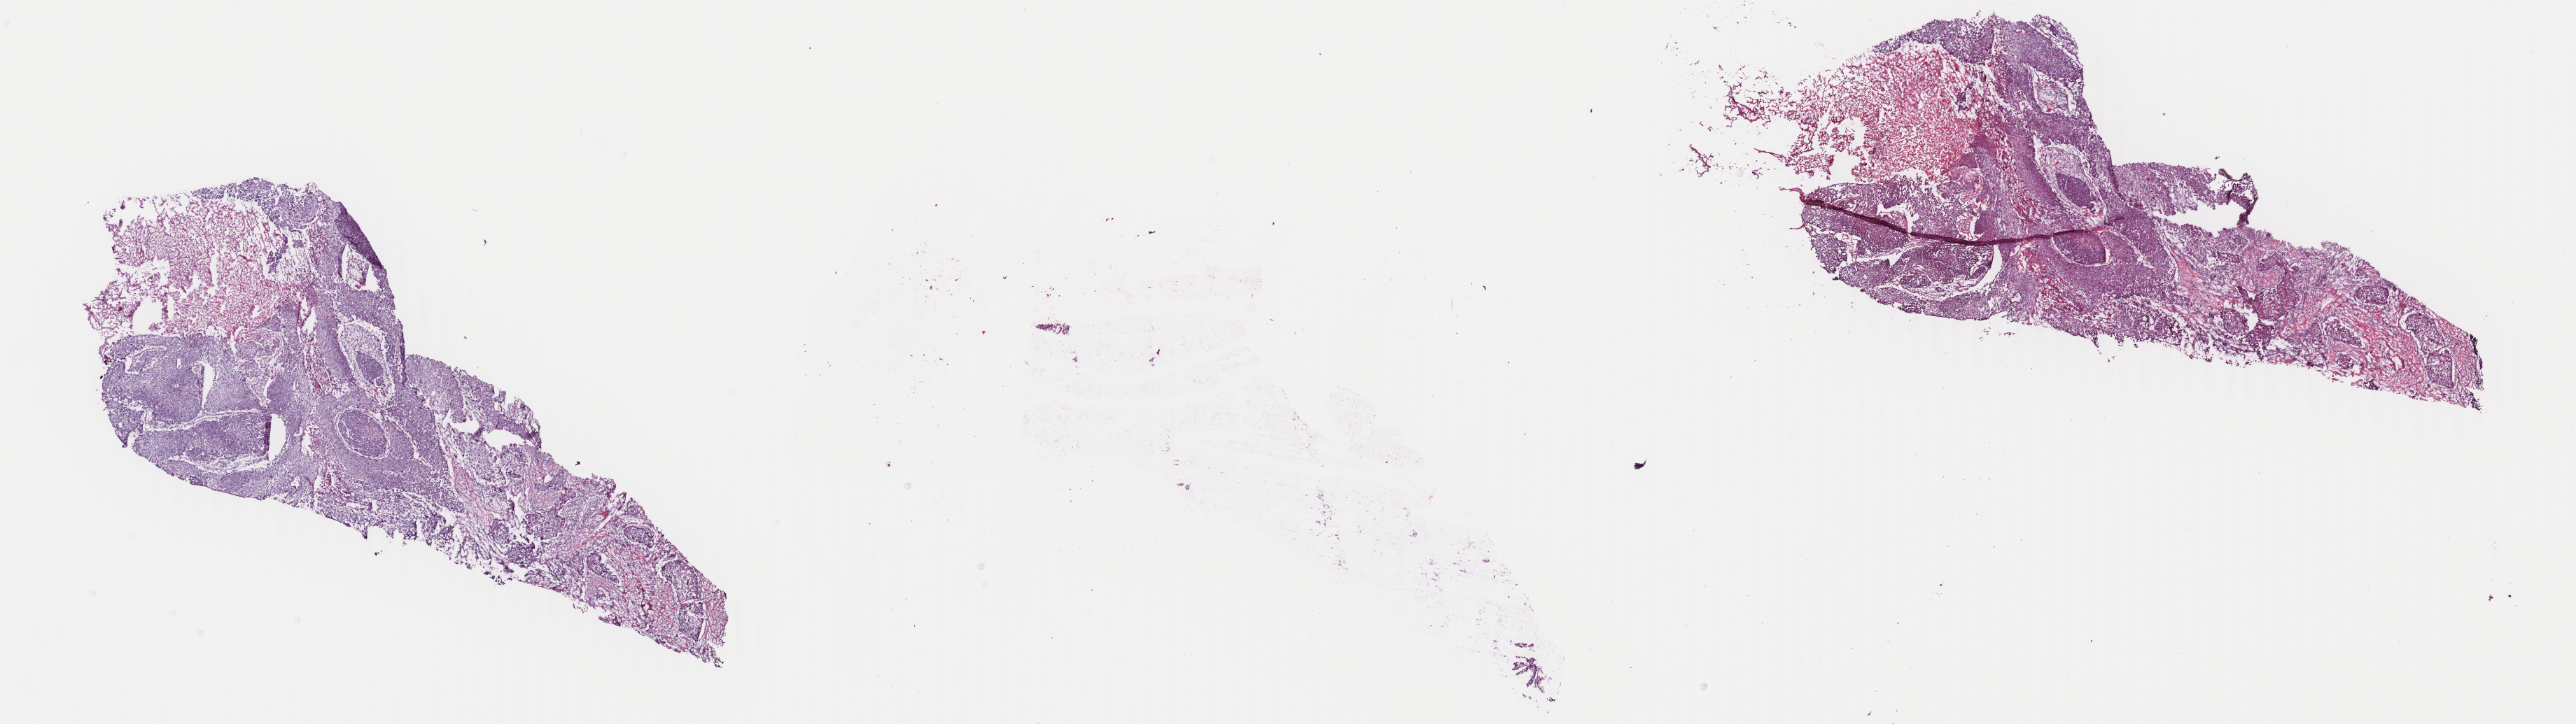
Whole-slide histology image, H&E-stained, shown as a low-resolution overview of the whole scanned area (about 29.3 x 8.2 mm, from a 40x scan), frozen section from the bottom of the tissue portion, sample: primary tumour, bladder. Male patient; age at initial diagnosis 71 years. Histologic grade: high grade. Pathologist review of this section (percent, as recorded): tumour cells 55%, tumour nuclei 75%, normal cells 10%, stromal cells 20%, necrosis 15%. Inflammatory infiltration, as recorded: lymphocyte infiltration 12%, monocyte infiltration 0%, neutrophil infiltration 3%.
- pathologic diagnosis: Transitional cell carcinoma
- AJCC pathologic stage: III (5th edition)